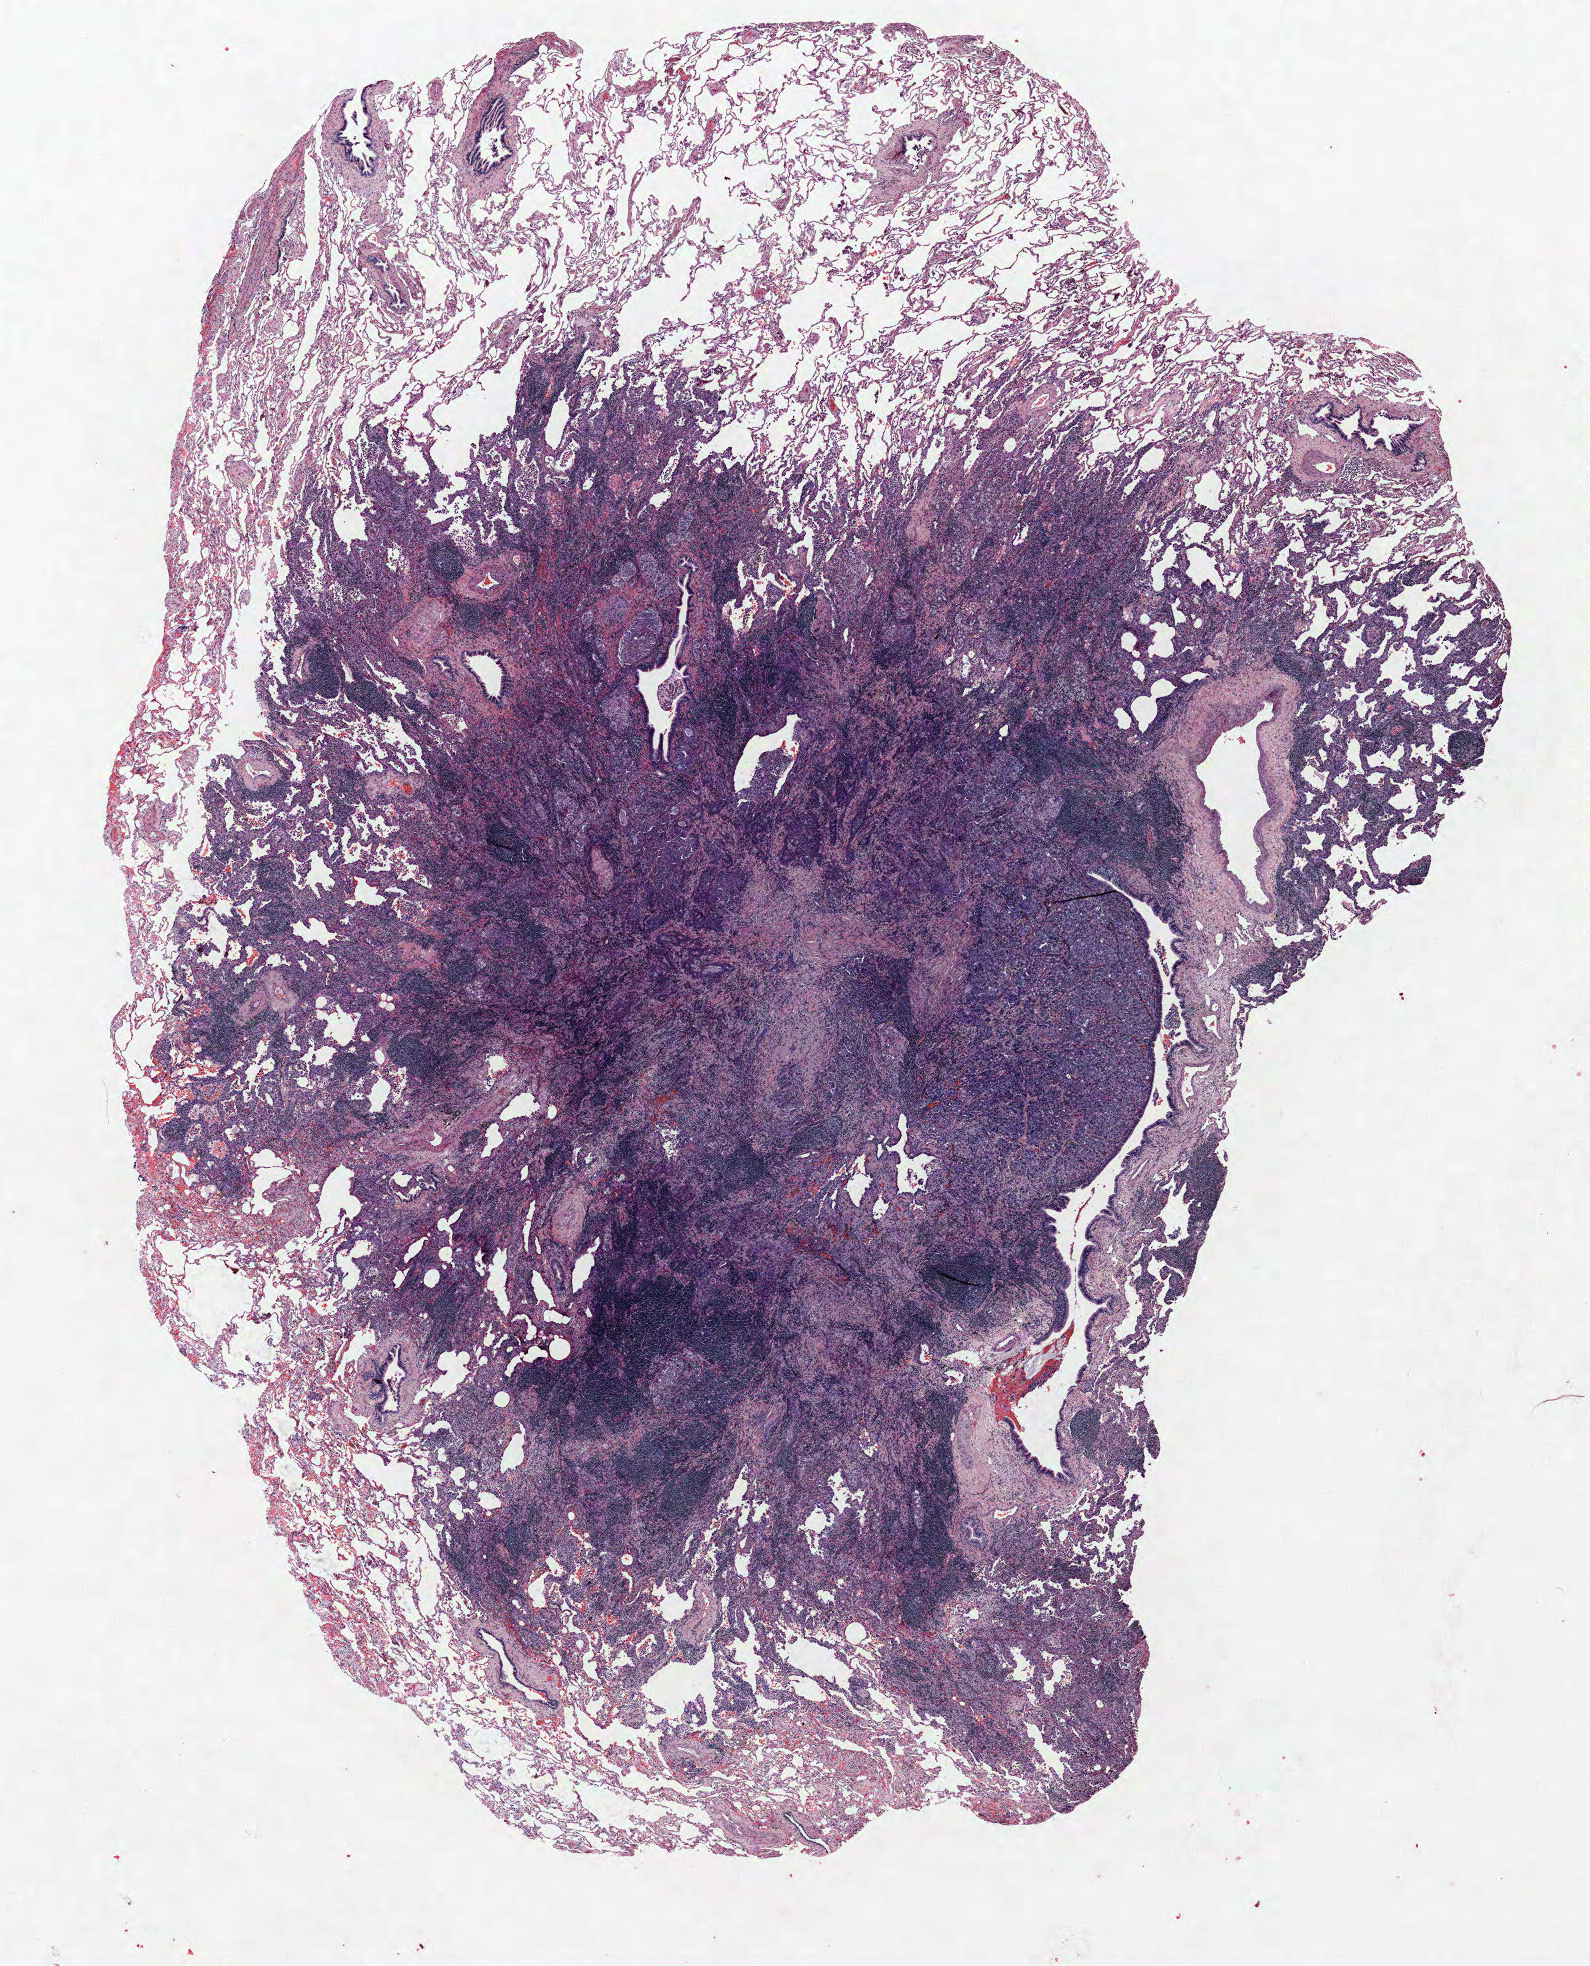
Whole-slide histology image, H&E — whole scanned area (about 12.7 x 15.7 mm, from a 40x scan) shown as a low-resolution overview, FFPE section, lung. Female patient, aged 71 at enrolment. Grade: moderately differentiated (G2).
Participant's lung-cancer diagnosis: Adenocarcinoma, NOS. Stage (AJCC 6th edition): IIA. Tumour size (pathology): 12 mm. Primary tumour location (clinical record): left upper lobe.